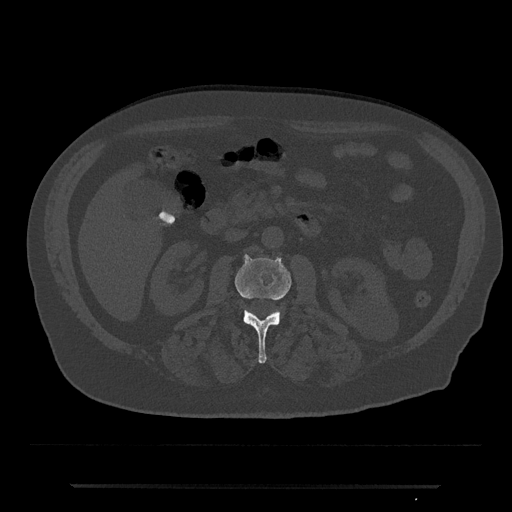
CT including the spine, one axial slice; position 461 of 797 along the scan axis; reconstruction kernel Br40s/3; bone window (W 1800 / L 400 HU); 0.5 mm slice thickness; 512 × 512 image matrix, field of view 434 × 434 mm. Patient: male, 80 years. Case-level facts recorded for this patient, not image findings: primary cancer: prostate.
Outlined on this slice (semi-automatically segmented with operator editing):
- L2 vertebra: bounding box <235,254,292,363> (left, top, right, bottom; pixels)